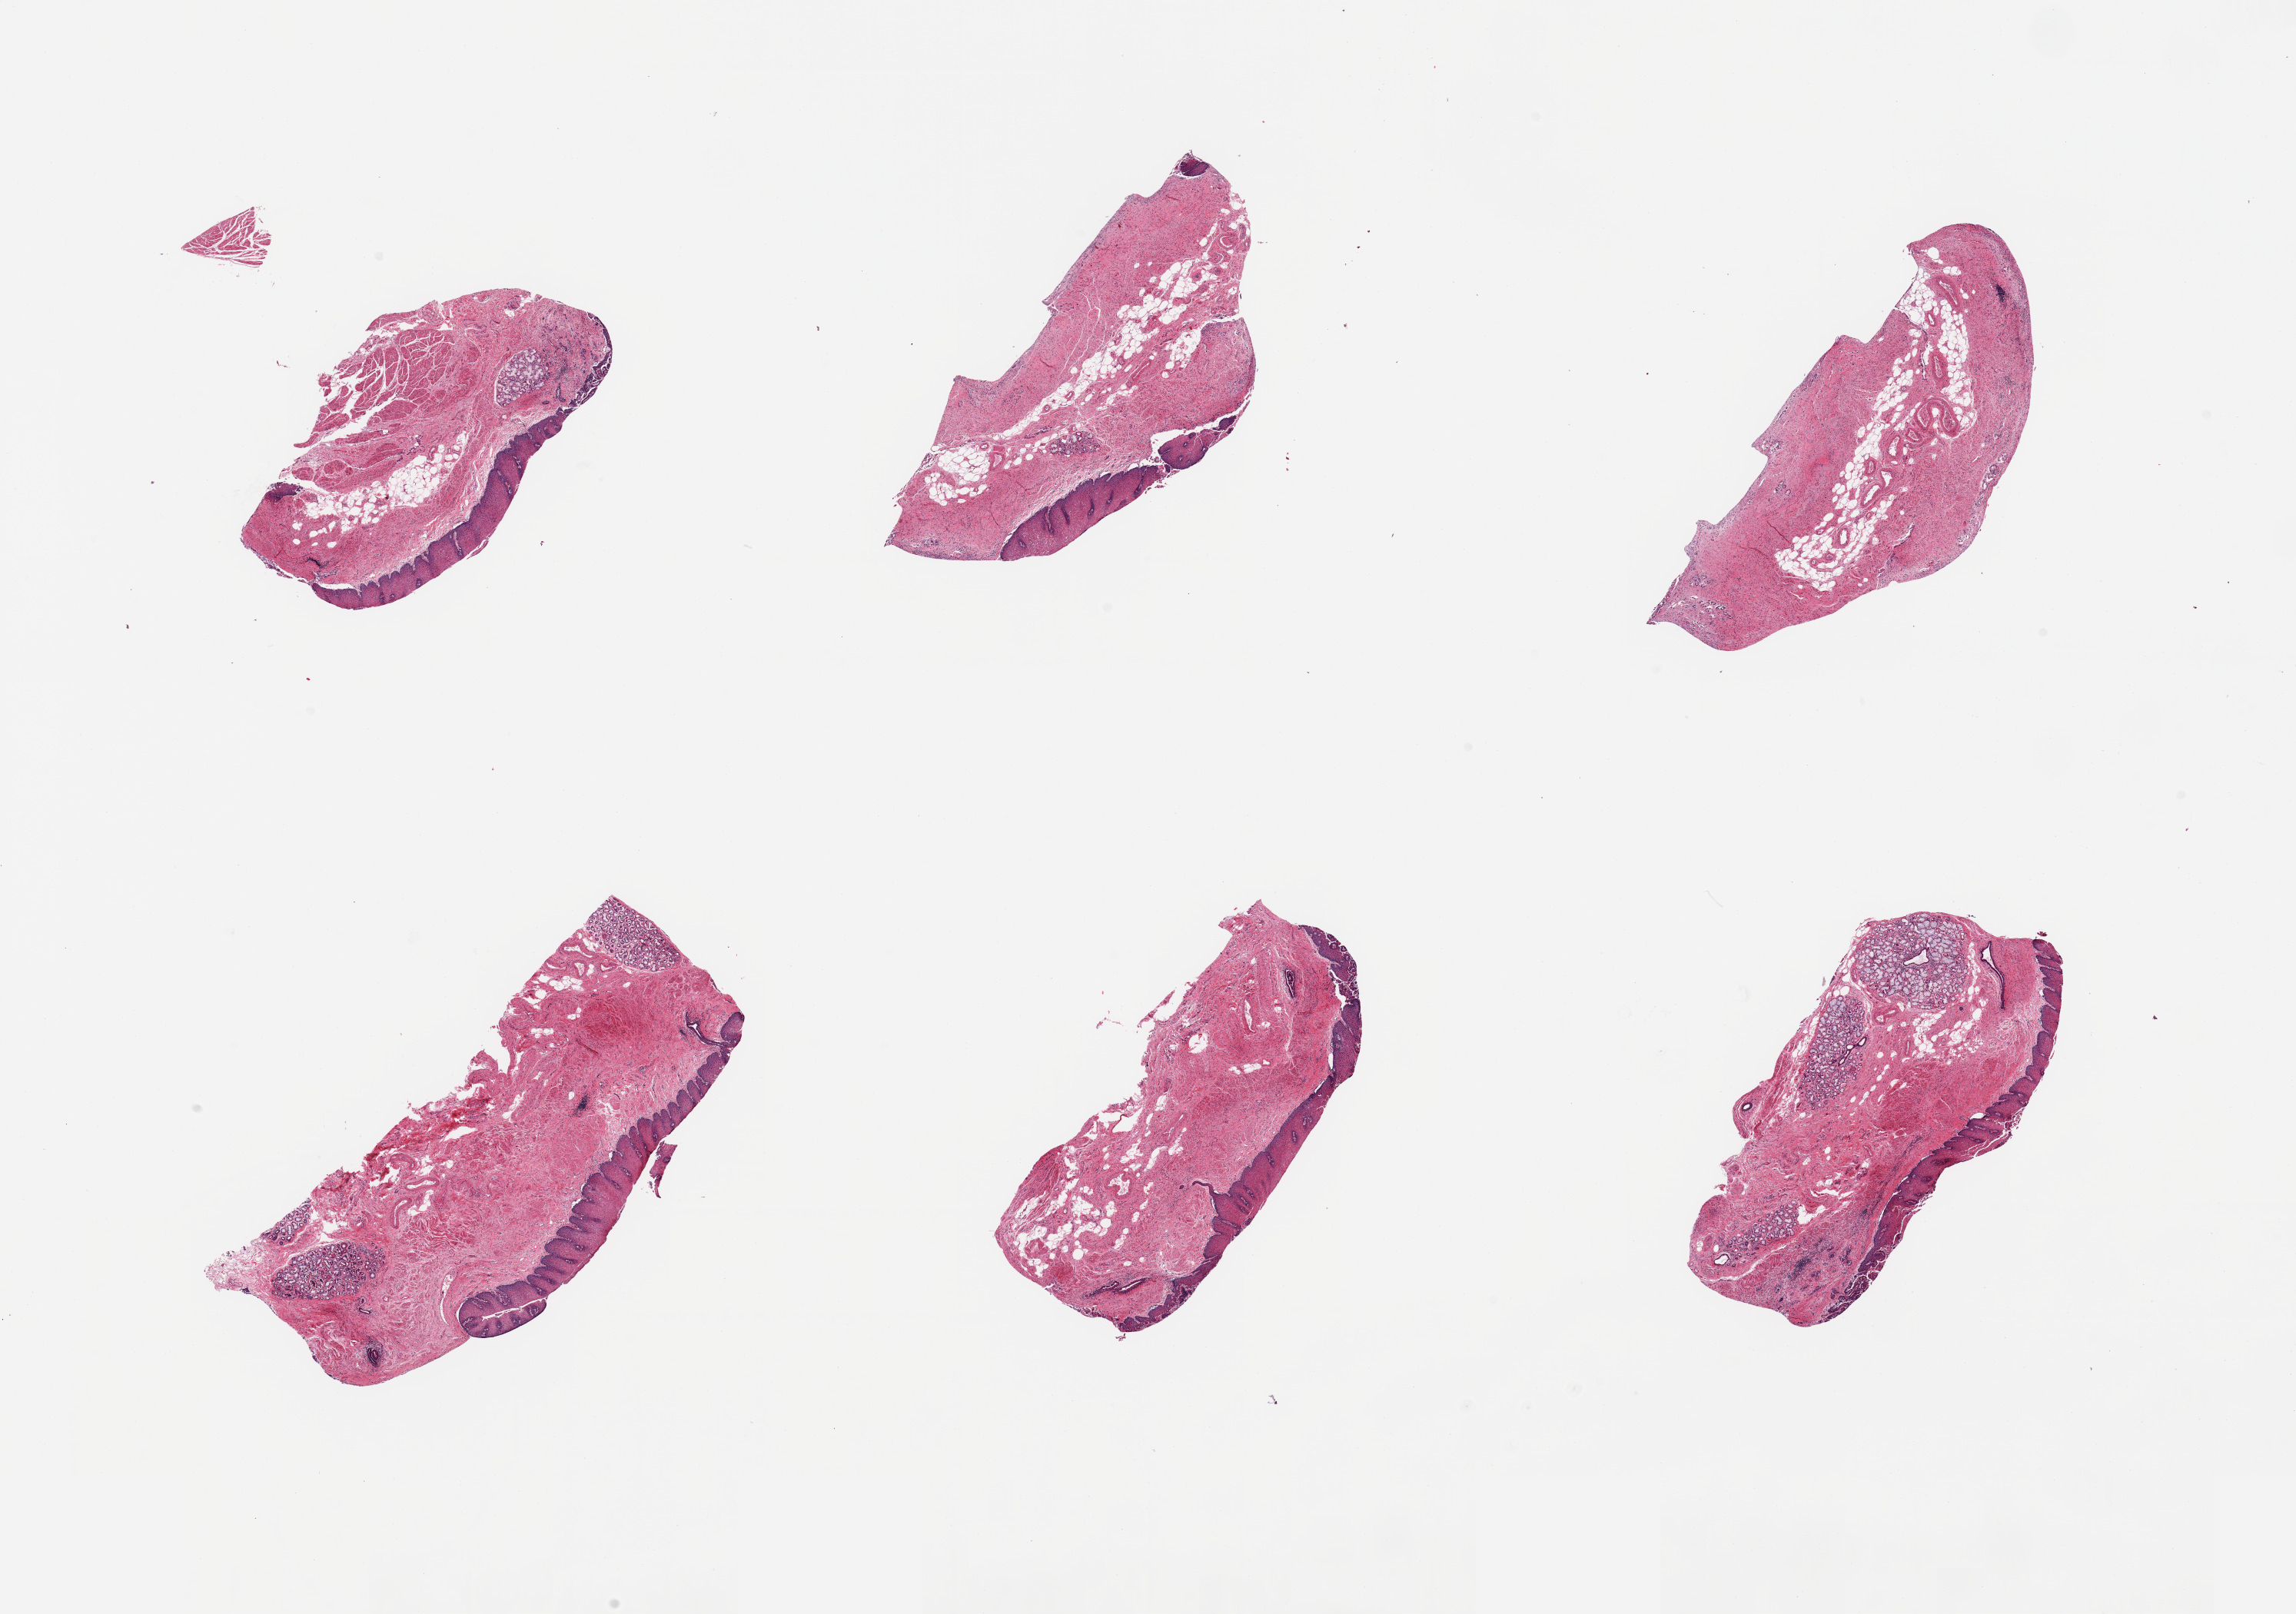
Digitized H&E-stained section, brightfield, shown as a low-resolution overview of the whole scanned area (about 23.6 x 16.6 mm); PAXgene-fixed, paraffin-embedded tissue; section of esophageal mucous membrane (target tissue); tissue donor sample. Male donor.
* reviewer comment on this tissue sample: 6 pieces; submucosal mucous glands up to 1 mm diameter in 3 pieces; epithelium partially sloughed in all; 1 piece without epithelium